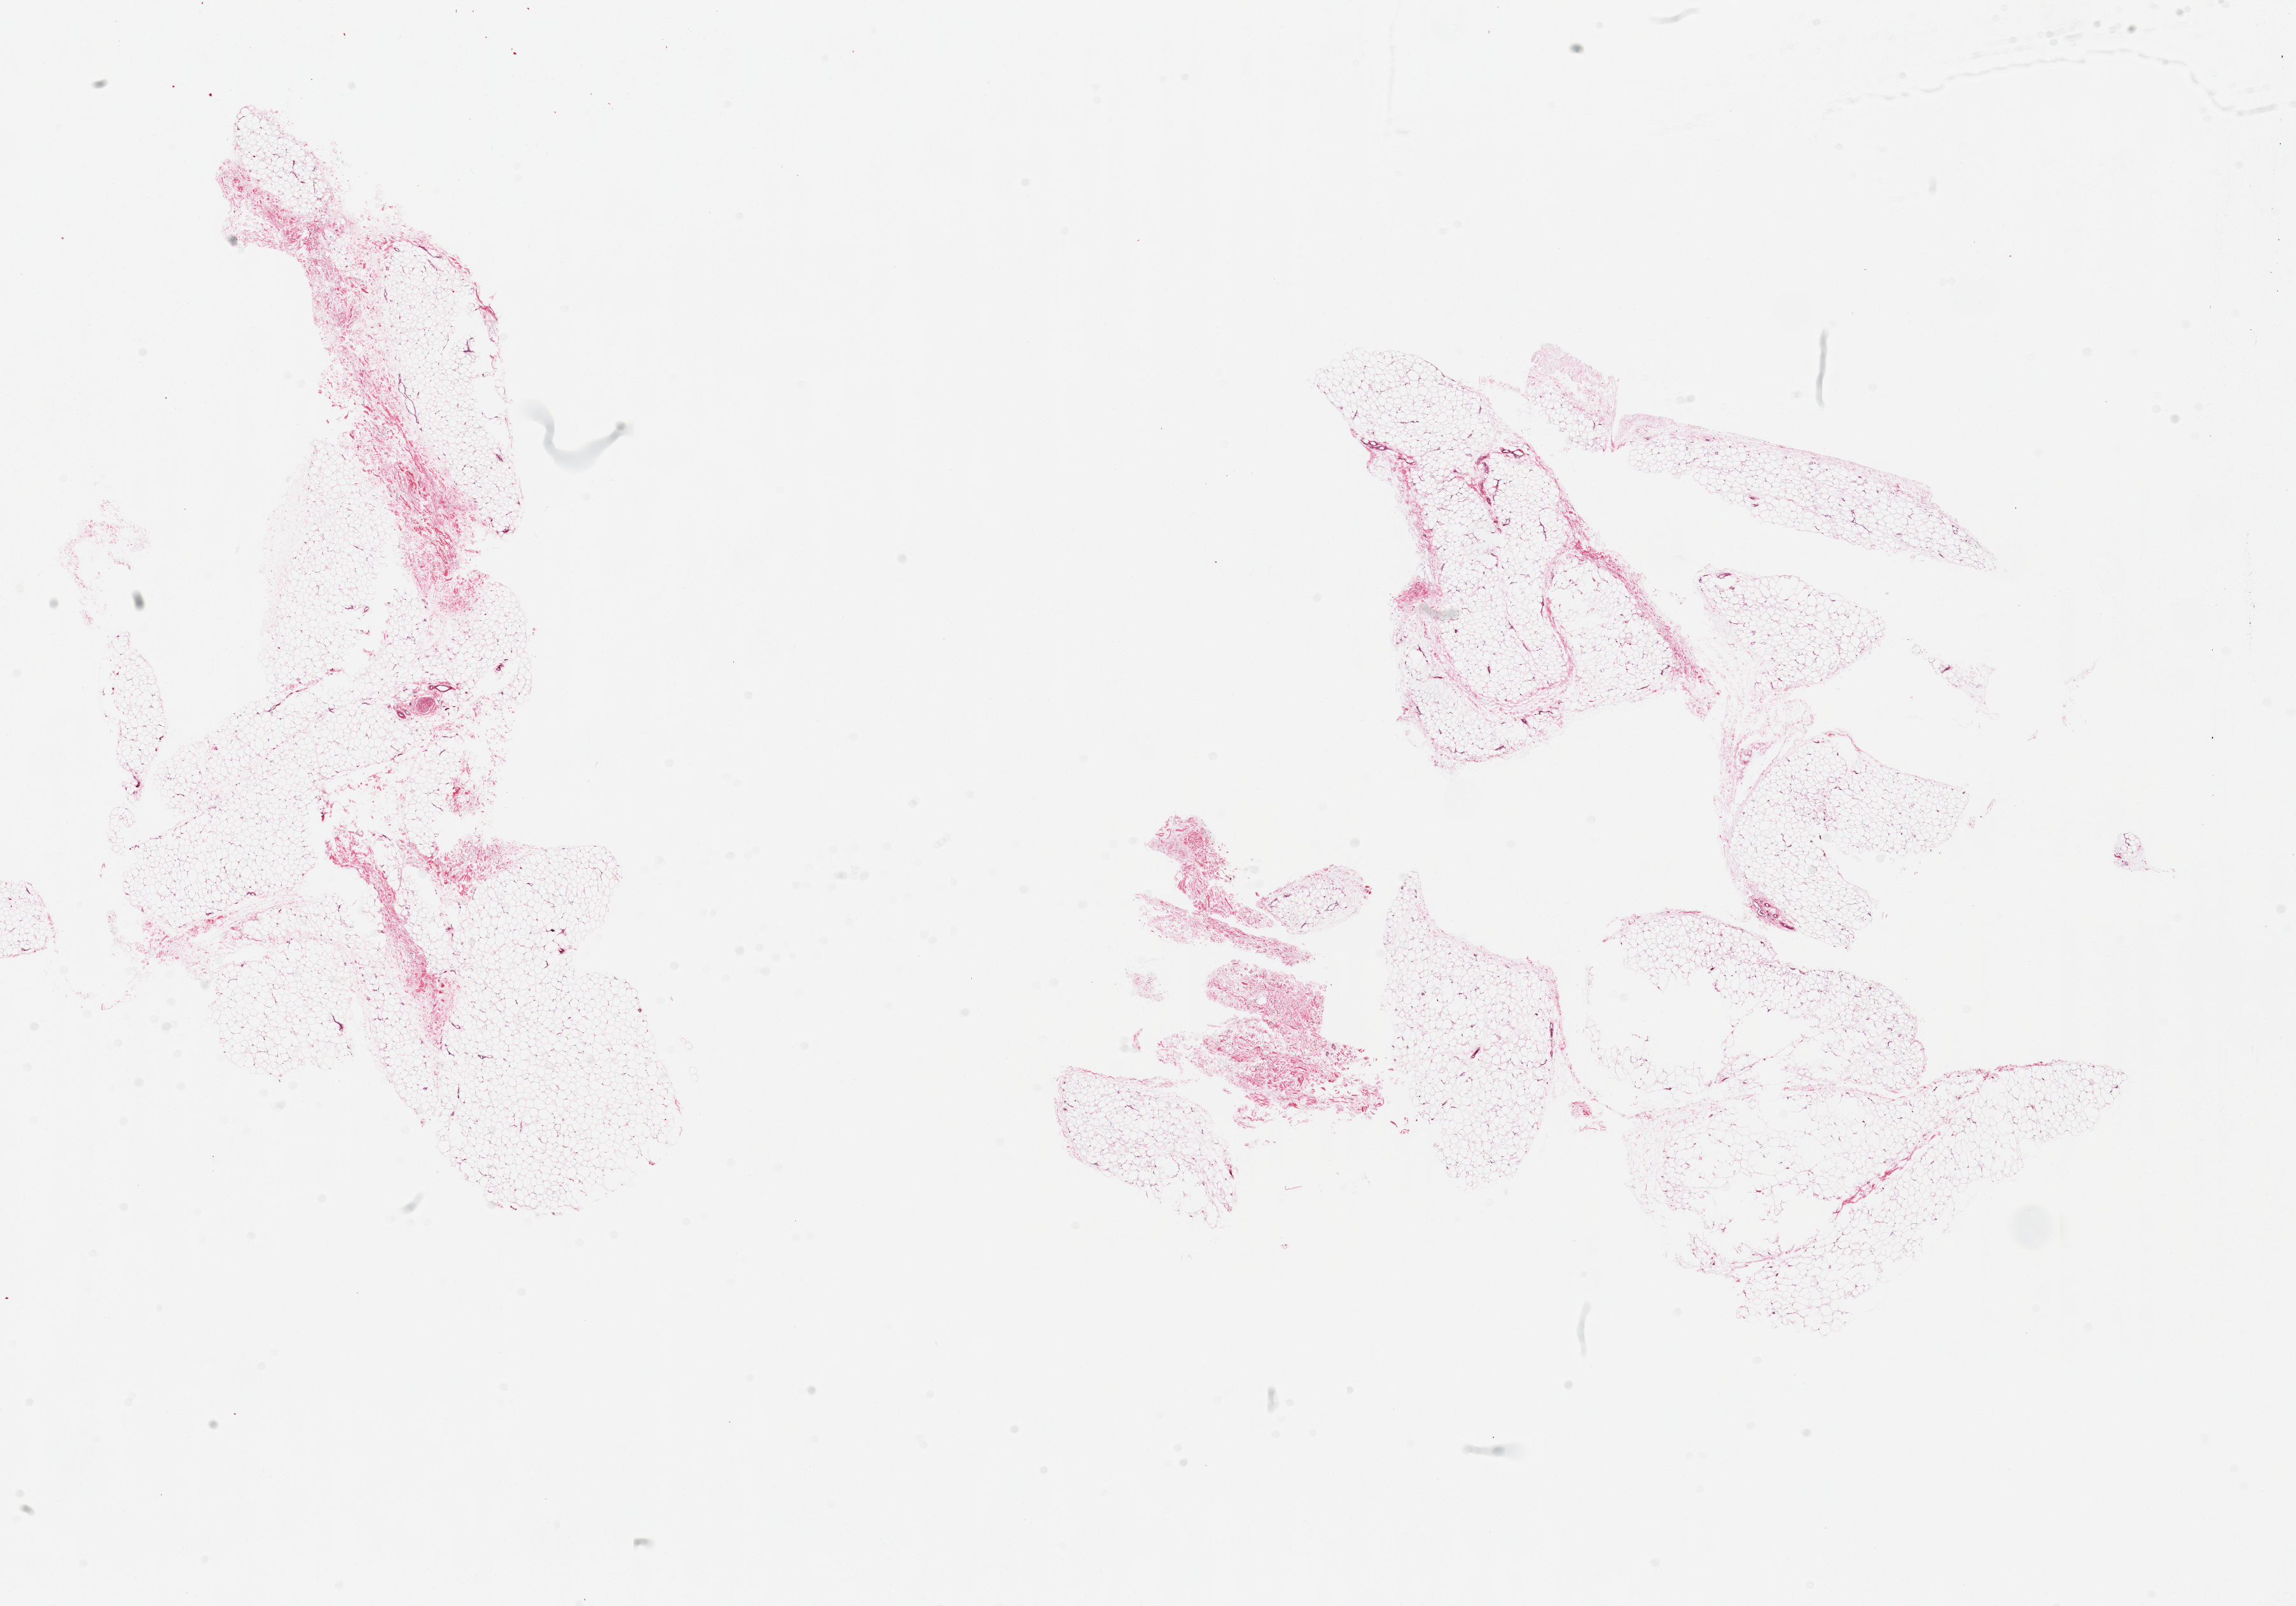
H&E whole-slide image — low-resolution overview of the scanned area, about 28.5 x 20.0 mm (from a 20x scan). PAXgene-fixed, paraffin-embedded tissue. Sampled site (target tissue): adipose tissue. Donor tissue sample. Donor sex: female.
Reviewer comment on this tissue sample: 2 pieces, minimal fibrous tissue (~10%).